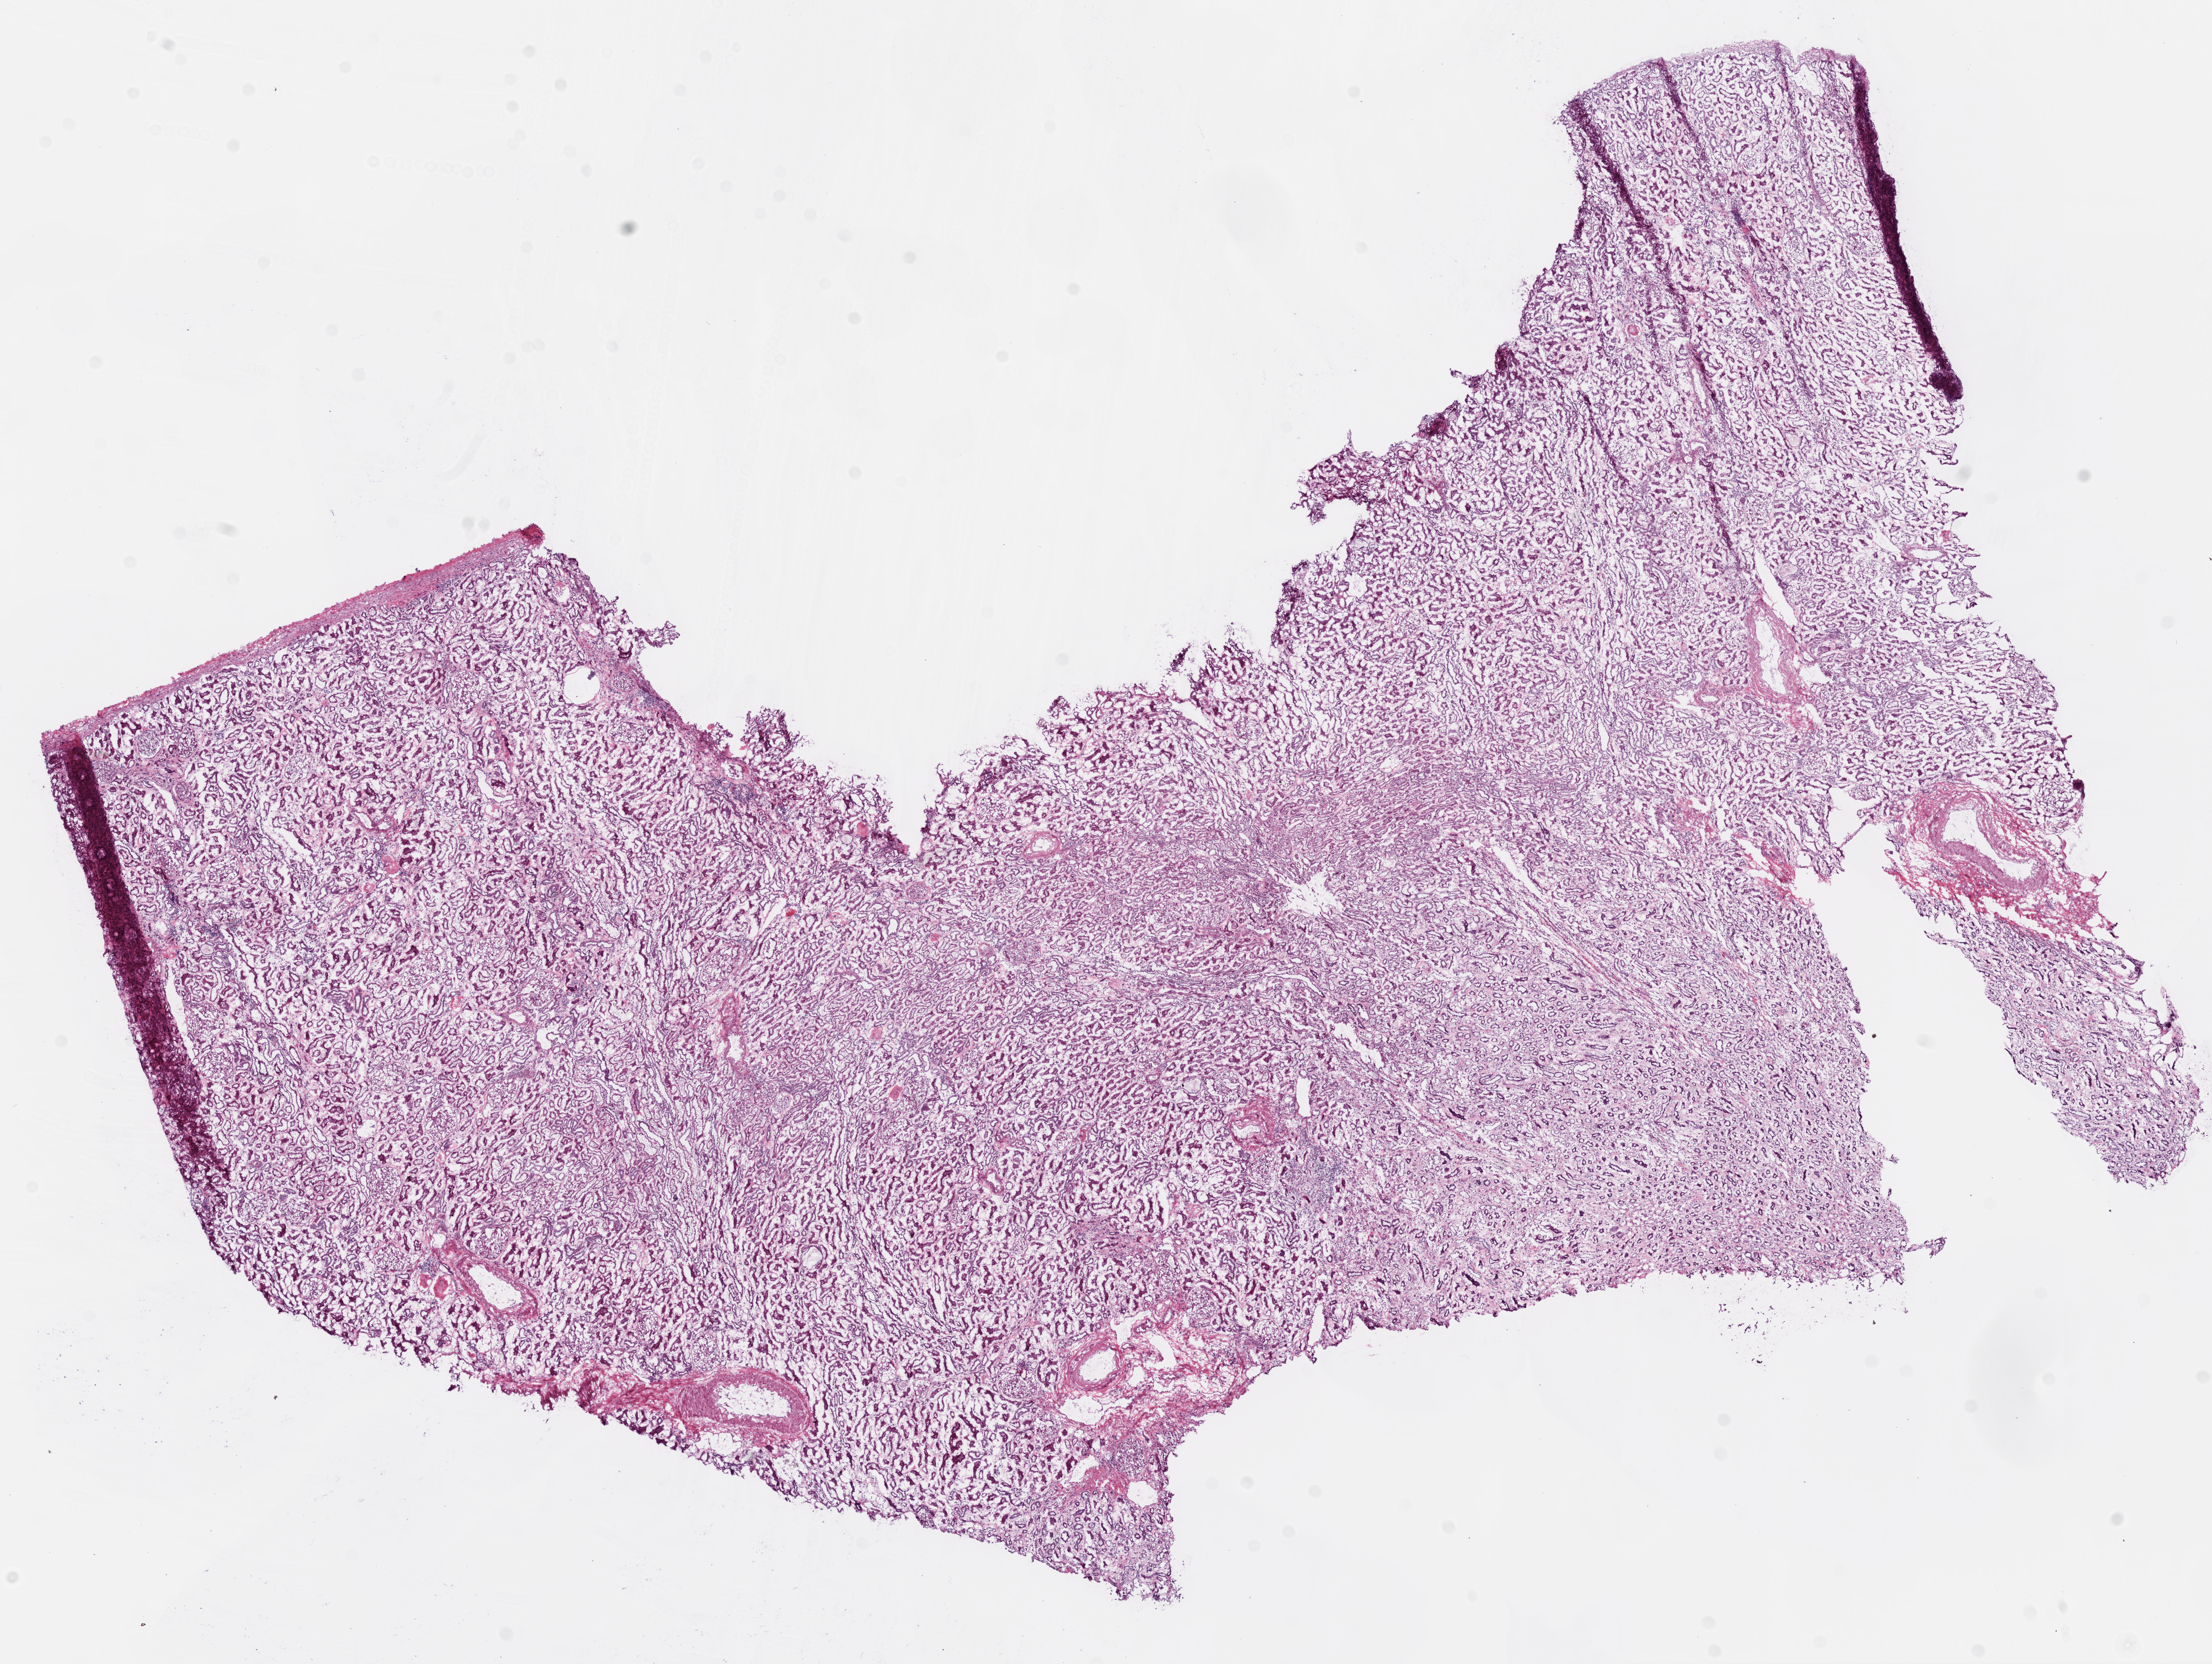
H&E-stained whole-slide image, shown as a low-resolution overview of the whole scanned area (about 15.0 x 11.3 mm). Frozen section from the top of the tissue portion. Sample: solid tissue normal (non-tumour tissue), kidney. Male patient; age at initial diagnosis 50 years.
This section: solid tissue normal (non-tumour) sample from the same patient. Patient diagnosis: Clear cell adenocarcinoma, NOS.